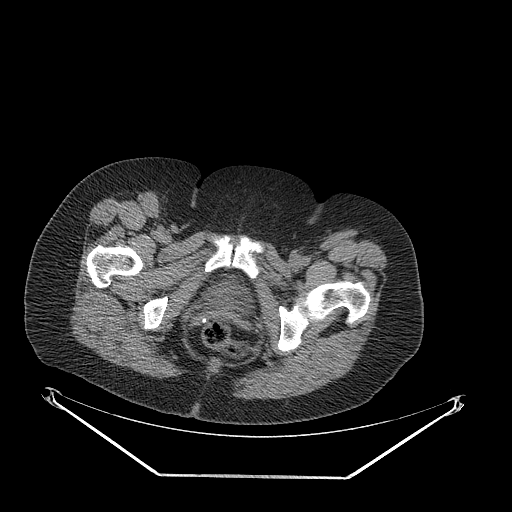
CT of an extremity soft-tissue mass (from a PET/CT study), one axial slice. Position 63 of 257 along the scan axis. Soft-tissue window (W 400 / L 40 HU). 3.75 mm slice thickness. 512 × 512 image matrix, field of view 500 × 500 mm. Female patient. From the clinical record (not read from this slice): histological type: synovial sarcoma; grade: intermediate; site of the primary tumour: right buttock.
Structures marked on this image (expert contour drawn on MRI and transferred to this co-registered scan by the dataset authors):
- gross tumour volume including surrounding oedema: bounding box [x1, y1, x2, y2] px = [112, 324, 126, 334]